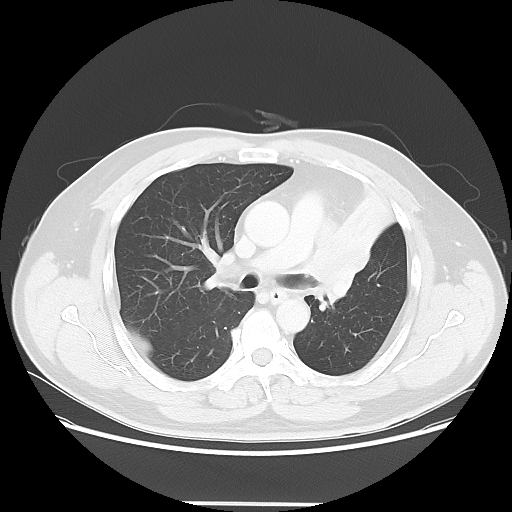
Chest CT, one axial slice. Slice 38 of 62 in the series (ordered by position). Lung window (W 1500 / L -600 HU). 5 mm slice thickness. 512 × 512 image matrix, field of view 403 × 403 mm. Patient: male, 49 years. From the clinical record (not read from this slice): clinical TNM (as recorded): T3 N3 M1c.
Outlined on this slice (rectangle marked by the reading radiologist):
- lung tumour (recorded histology: squamous cell carcinoma): bounding box [x1, y1, x2, y2] px = [297, 199, 366, 305]